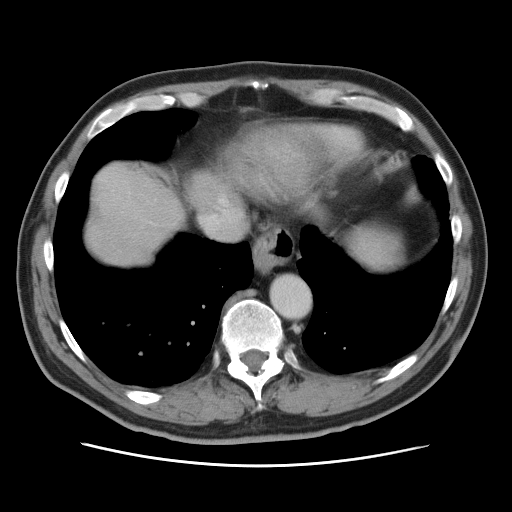
Contrast-enhanced abdominal CT, one axial slice. Position 71 of 80 along the scan axis. 120 kVp. Intravenous contrast given. Soft-tissue window (W 400 / L 40 HU). 5 mm slice thickness. 512 × 512 image matrix, field of view 370 × 370 mm. Male patient, age 69 years. From the clinical record (not read from this slice): diagnosis: colorectal cancer liver metastases, imaged before liver resection; multiple liver metastases: no; largest metastasis: 5 cm; chemotherapy before resection: no.
Annotated regions visible in this slice (manually delineated by an expert):
- hepatic veins: bounding box (x1, y1, x2, y2) in pixels: (119, 180, 236, 233)
- liver: (85, 165, 180, 265)
- planned liver remnant (the part of the liver to remain after resection): (85, 211, 173, 265)